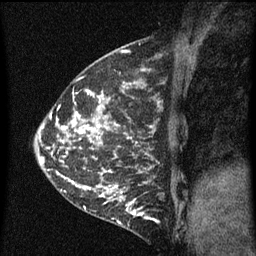
Breast MRI (dynamic contrast-enhanced), one sagittal slice; slice 17 of 60 in the series (ordered by position); dynamic contrast-enhanced series, image 2 of 5 at this slice position (ordered by acquisition); 1.5 T; TE 4.2 ms, TR 8 ms; 256 × 256 image matrix, field of view 180 × 180 mm. Patient: female, 35 years.
Annotated regions visible in this slice (semi-automatic segmentation, software-assisted and operator-edited):
- analysis volume of interest (the breast-tissue region the enhancement analysis was run in; not a lesion): bounding box (x1, y1, x2, y2) in pixels: (118, 190, 158, 229)
- tumour enhancement mask (voxels above the 70 % enhancement threshold inside the analysis volume of interest): (120, 196, 158, 223)